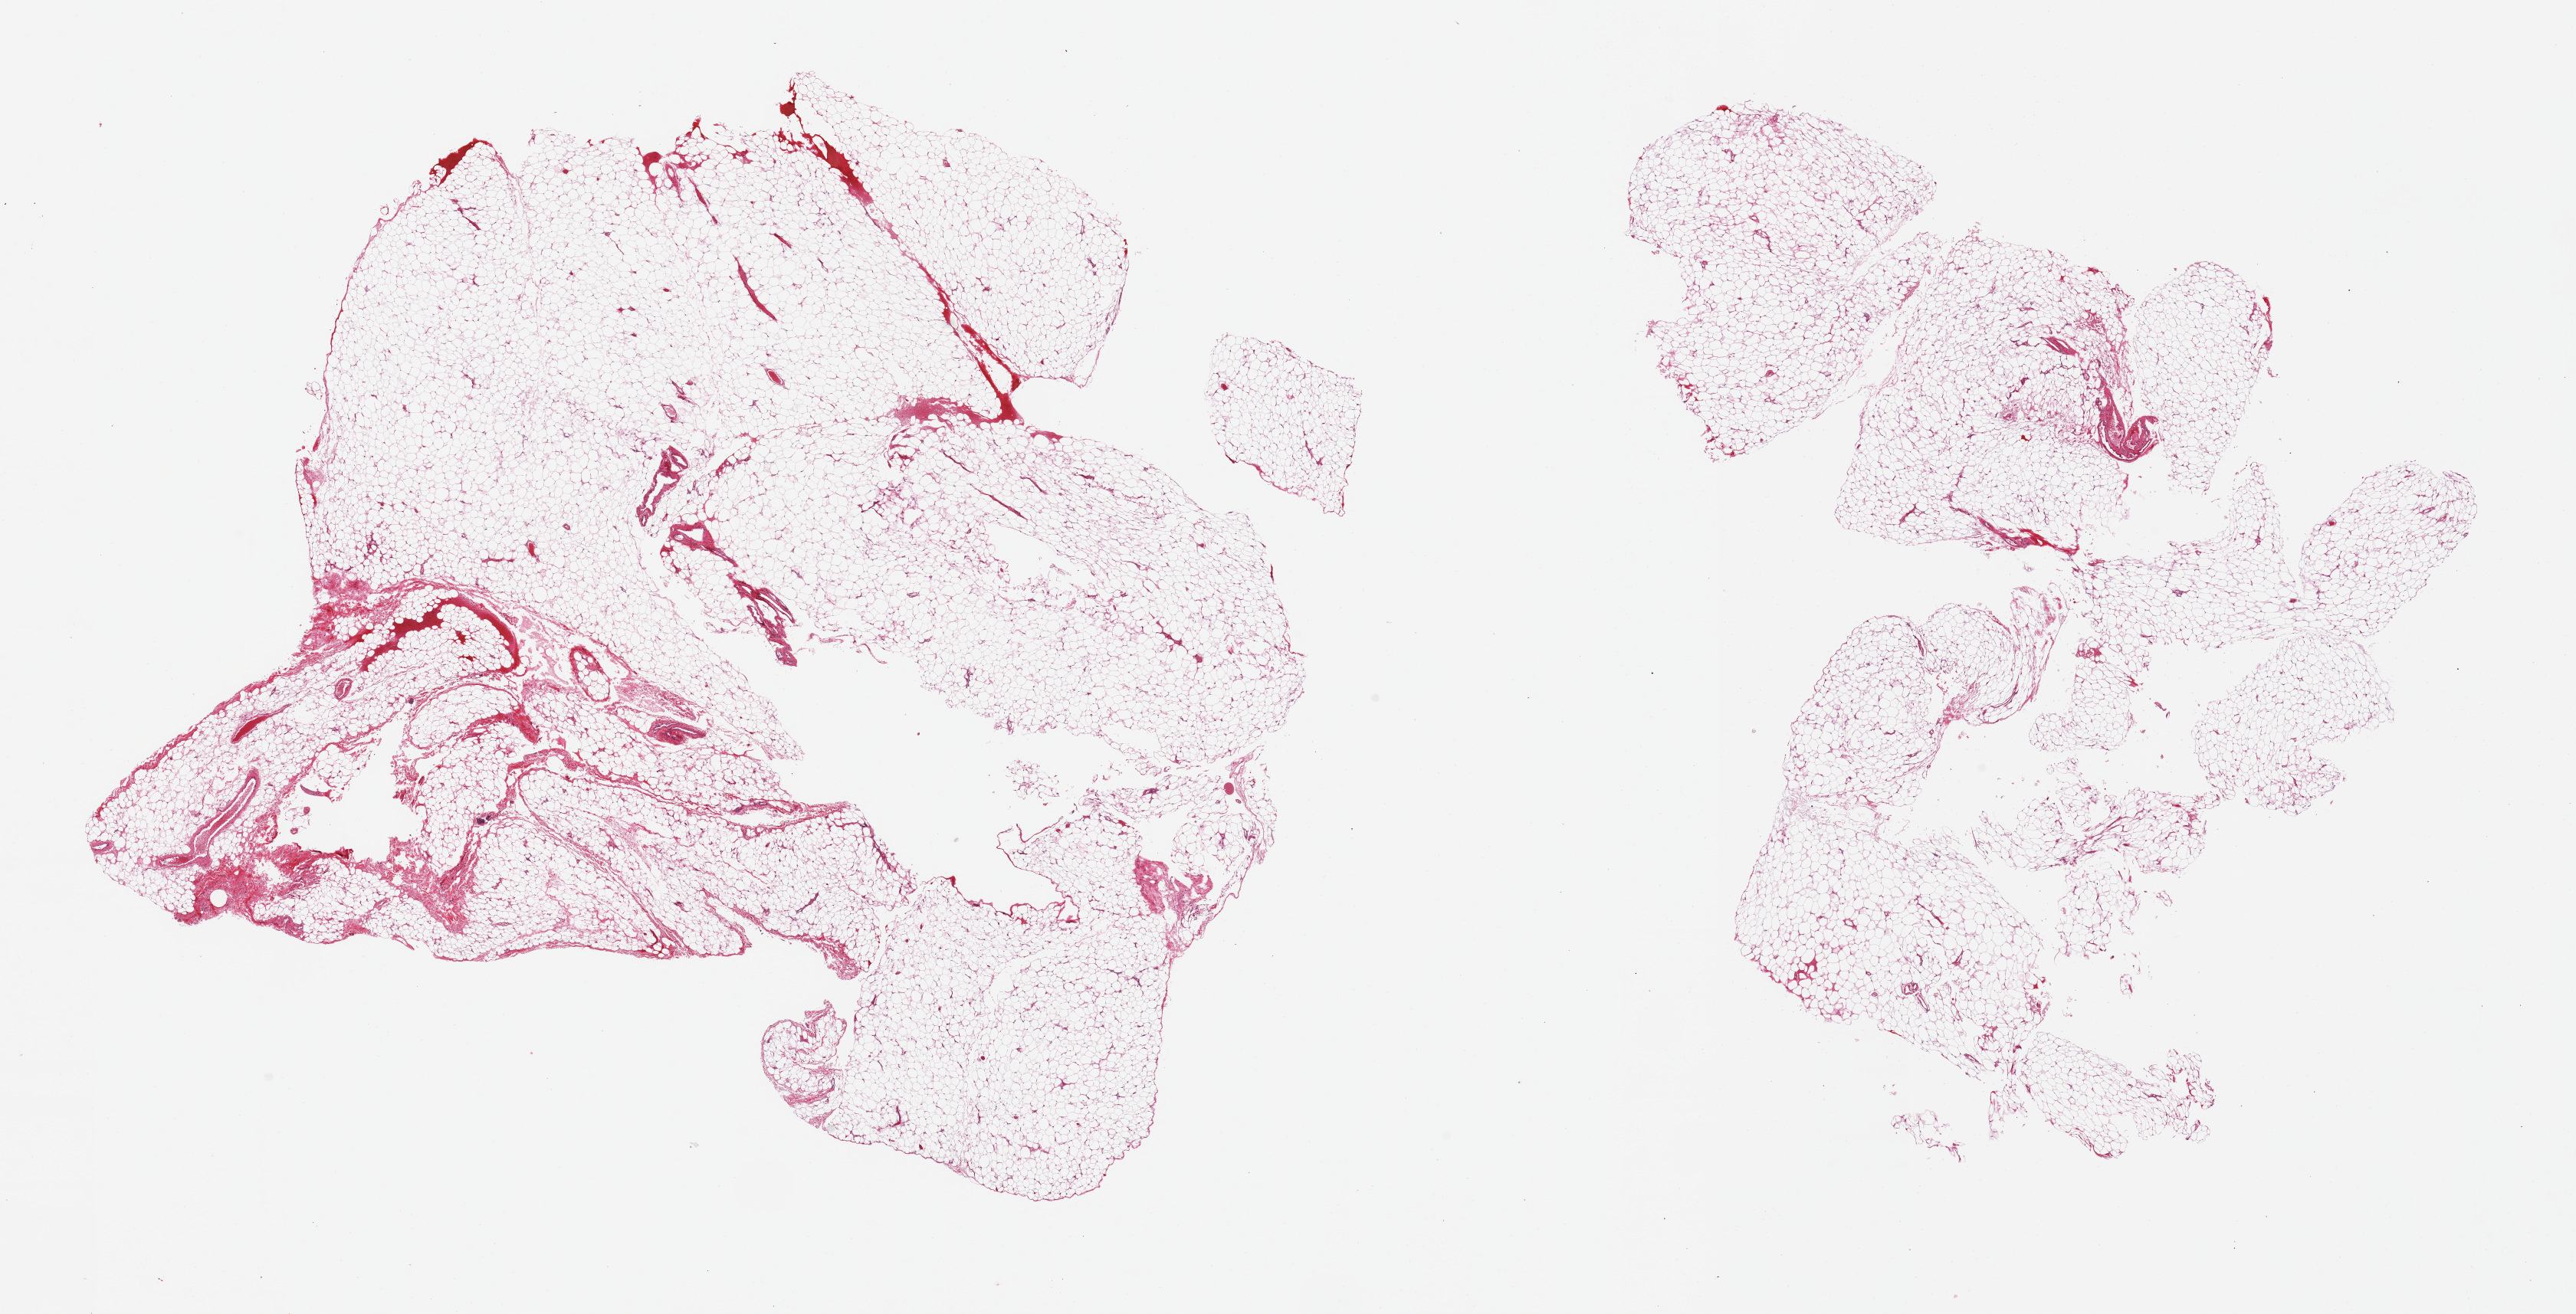
H&E whole-slide image, brightfield — a low-resolution overview of the entire scanned area, about 26.6 x 13.6 mm, PAXgene-fixed paraffin-embedded (PFPE) section, sampled site (target tissue): pancreas, tissue donor sample.
Reviewer comment on this tissue sample: 2 pieces, adipose tissue, no pancratic parenchyma.